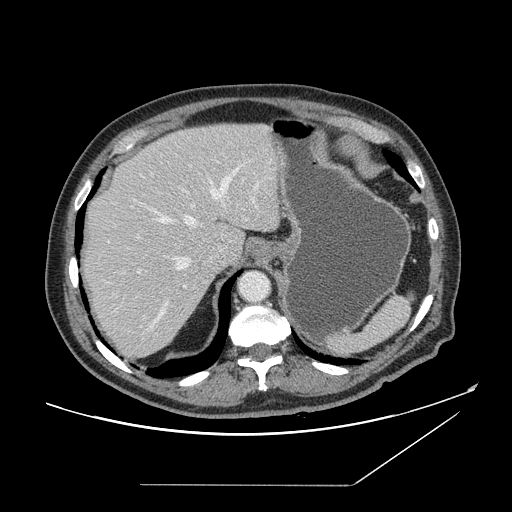
Contrast-enhanced abdominal CT, one axial slice; position 120 of 166 along the scan axis; 120 kVp; intravenous contrast given; soft-tissue window (W 400 / L 40 HU); 512 × 512 image matrix, field of view 416 × 416 mm. Male patient, age 80 years. From the clinical record (not read from this slice): diagnosis: colorectal cancer liver metastases, imaged before liver resection; multiple liver metastases: no; largest metastasis: 2.2 cm; disease in both lobes: no.
Structures marked on this image (expert manual segmentation):
- hepatic veins: bounding box (x1, y1, x2, y2) in pixels: (151, 166, 241, 328)
- liver: (81, 123, 280, 358)
- planned liver remnant (the part of the liver to remain after resection): (84, 123, 280, 261)
- portal vein (with intrahepatic branches): (137, 184, 260, 273)